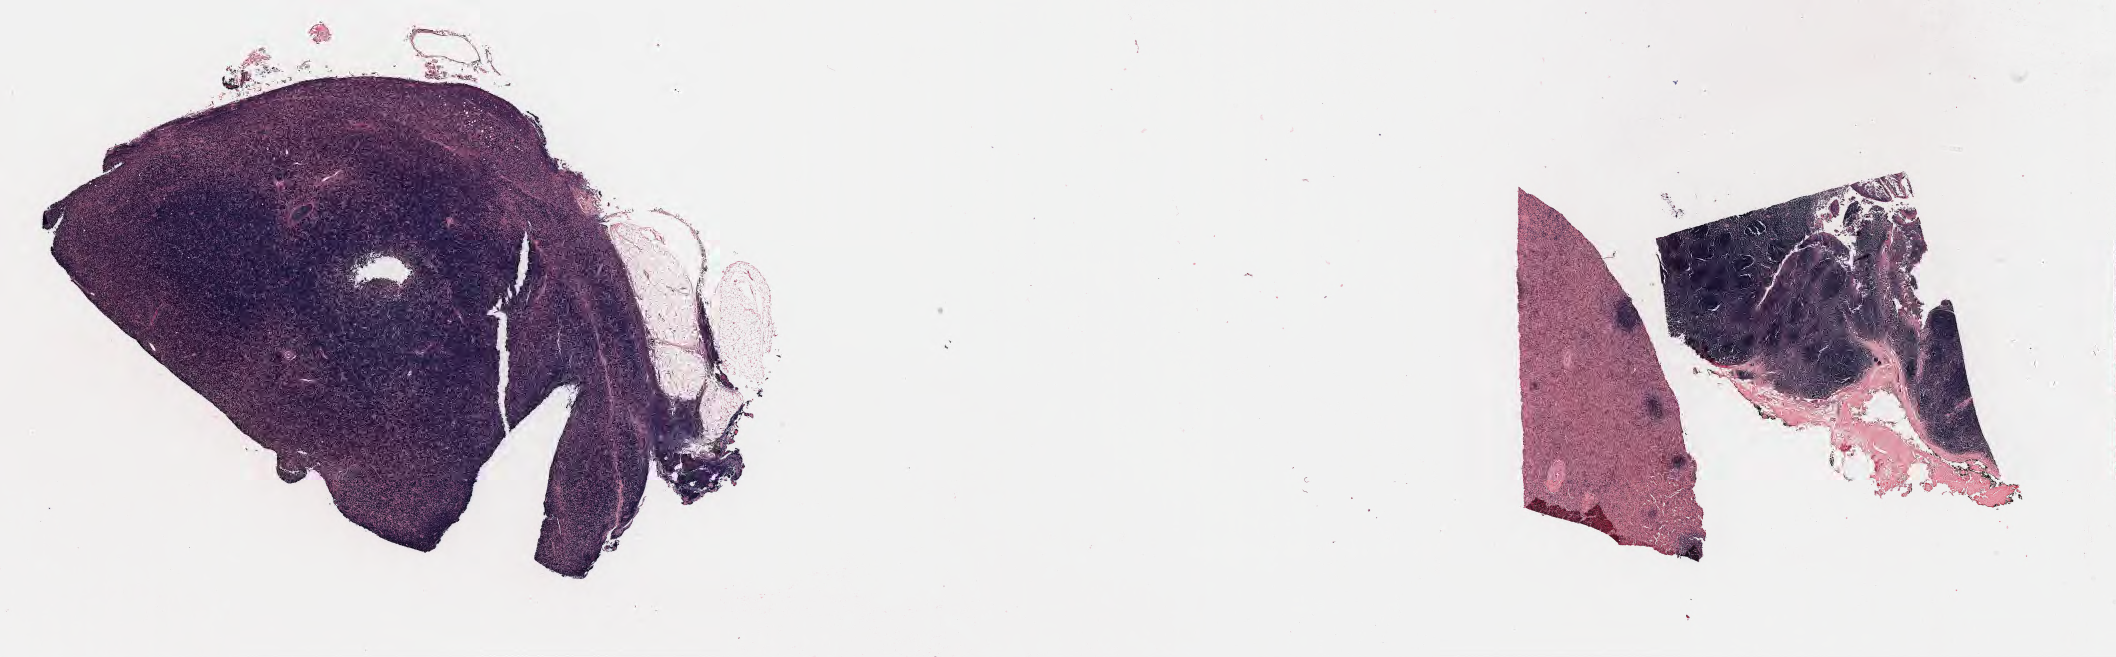
Whole-slide image; stain recorded as Iodonitrotetrazolium, a low-resolution overview of the entire scanned area, about 34.2 x 10.6 mm; specimen: tumor tissue; anatomic site: lymph node. Patient male; age 26 years.
Diagnosis: Diffuse large B-cell lymphoma, NOS.